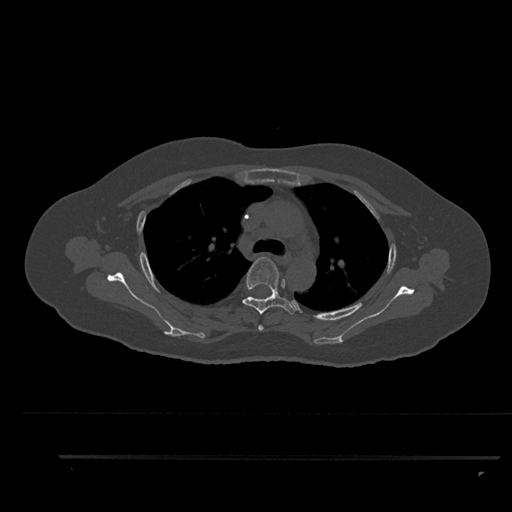
CT including the spine, one axial slice. Position 645 of 797 along the scan axis. 120 kVp. Bone window (W 1800 / L 400 HU). 512 × 512 image matrix, field of view 408 × 408 mm. Patient: female, 44 years. Case-level facts recorded for this patient, not image findings: primary cancer: renal; vertebrae with lytic lesions (as recorded): L1.
Outlined on this slice (semi-automatically segmented with operator editing):
- T3 vertebra: box from (x=258, y=325) to (x=264, y=331) px
- T4 vertebra: (x=242, y=257)–(x=297, y=315)